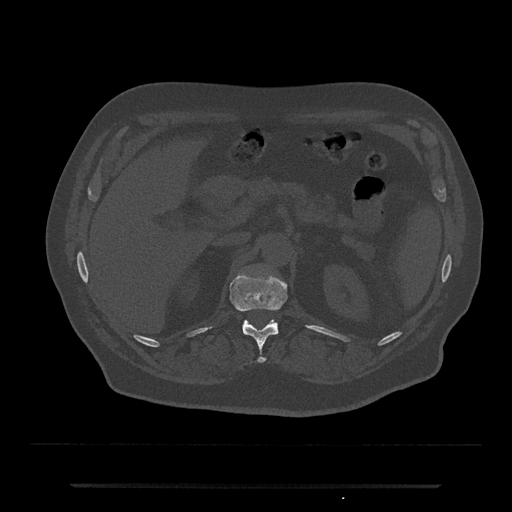
CT including the spine, one axial slice; position 584 of 797 along the scan axis; reconstruction kernel Br40s/3; bone window (W 1800 / L 400 HU); 512 × 512 image matrix. Patient: male, 80 years. Case-level facts recorded for this patient, not image findings: primary cancer: prostate; vertebrae with lytic lesions (as recorded): L1, T11.
Outlined on this slice (semi-automatic segmentation, software-assisted and operator-edited):
- T12 vertebra: bounding box <229,274,288,363> (left, top, right, bottom; pixels)